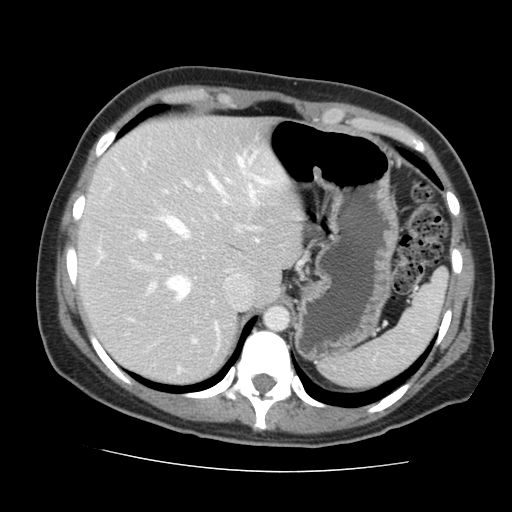
Contrast-enhanced abdominal CT, one axial slice; 120 kVp; intravenous contrast given; soft-tissue window (W 400 / L 40 HU); 2.5 mm slice thickness; 512 × 512 image matrix. Female patient, age 46 years. Case-level facts recorded for this patient, not image findings: diagnosis: colorectal cancer liver metastases, imaged before liver resection.
Outlined on this slice (expert manual segmentation):
- hepatic veins: bounding box <144,158,254,300> (left, top, right, bottom; pixels)
- liver: <80,118,298,382>
- planned liver remnant (the part of the liver to remain after resection): <80,118,298,382>
- portal vein (with intrahepatic branches): <98,178,251,343>